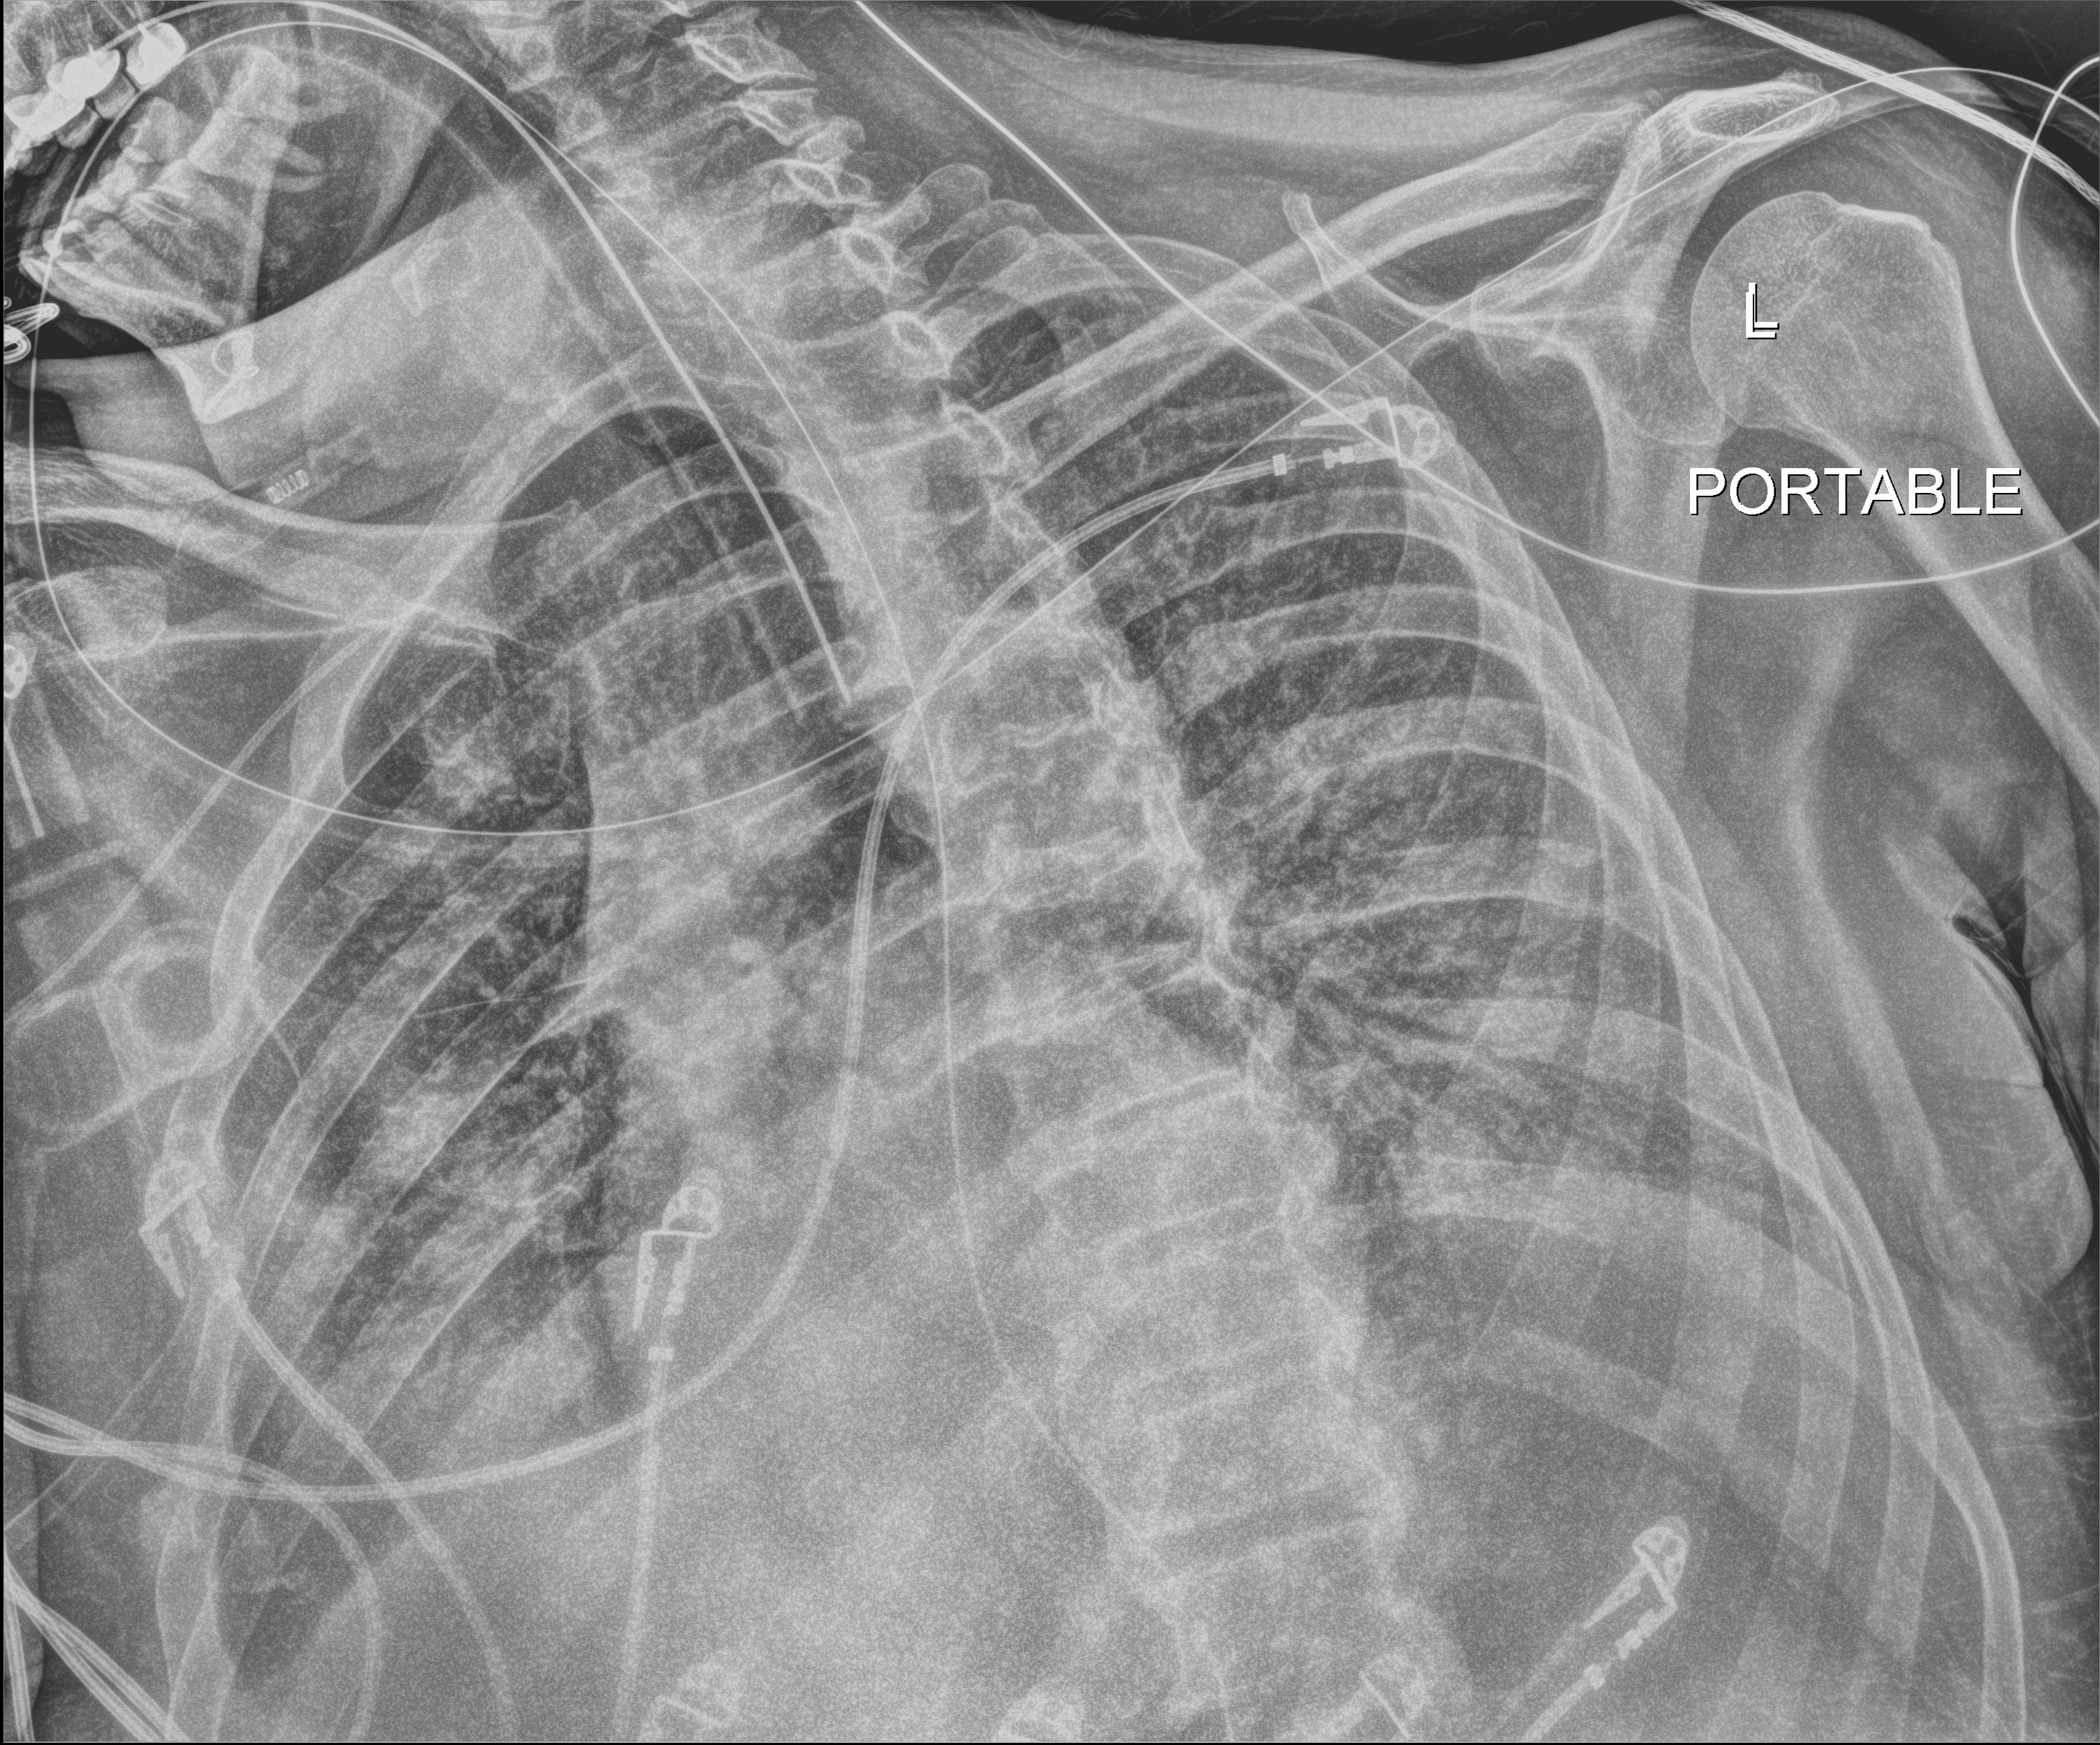
Chest X-ray (portable), anteroposterior (AP) projection. Male patient hospitalised with COVID-19, age 60–74 years.
Admission-level facts for this patient (not findings on this image; timing relative to this image not recorded):
- other chronic lung disease (admission record): no
- admitted to intensive care during this hospital stay: yes
- mechanically ventilated during this hospital stay: yes